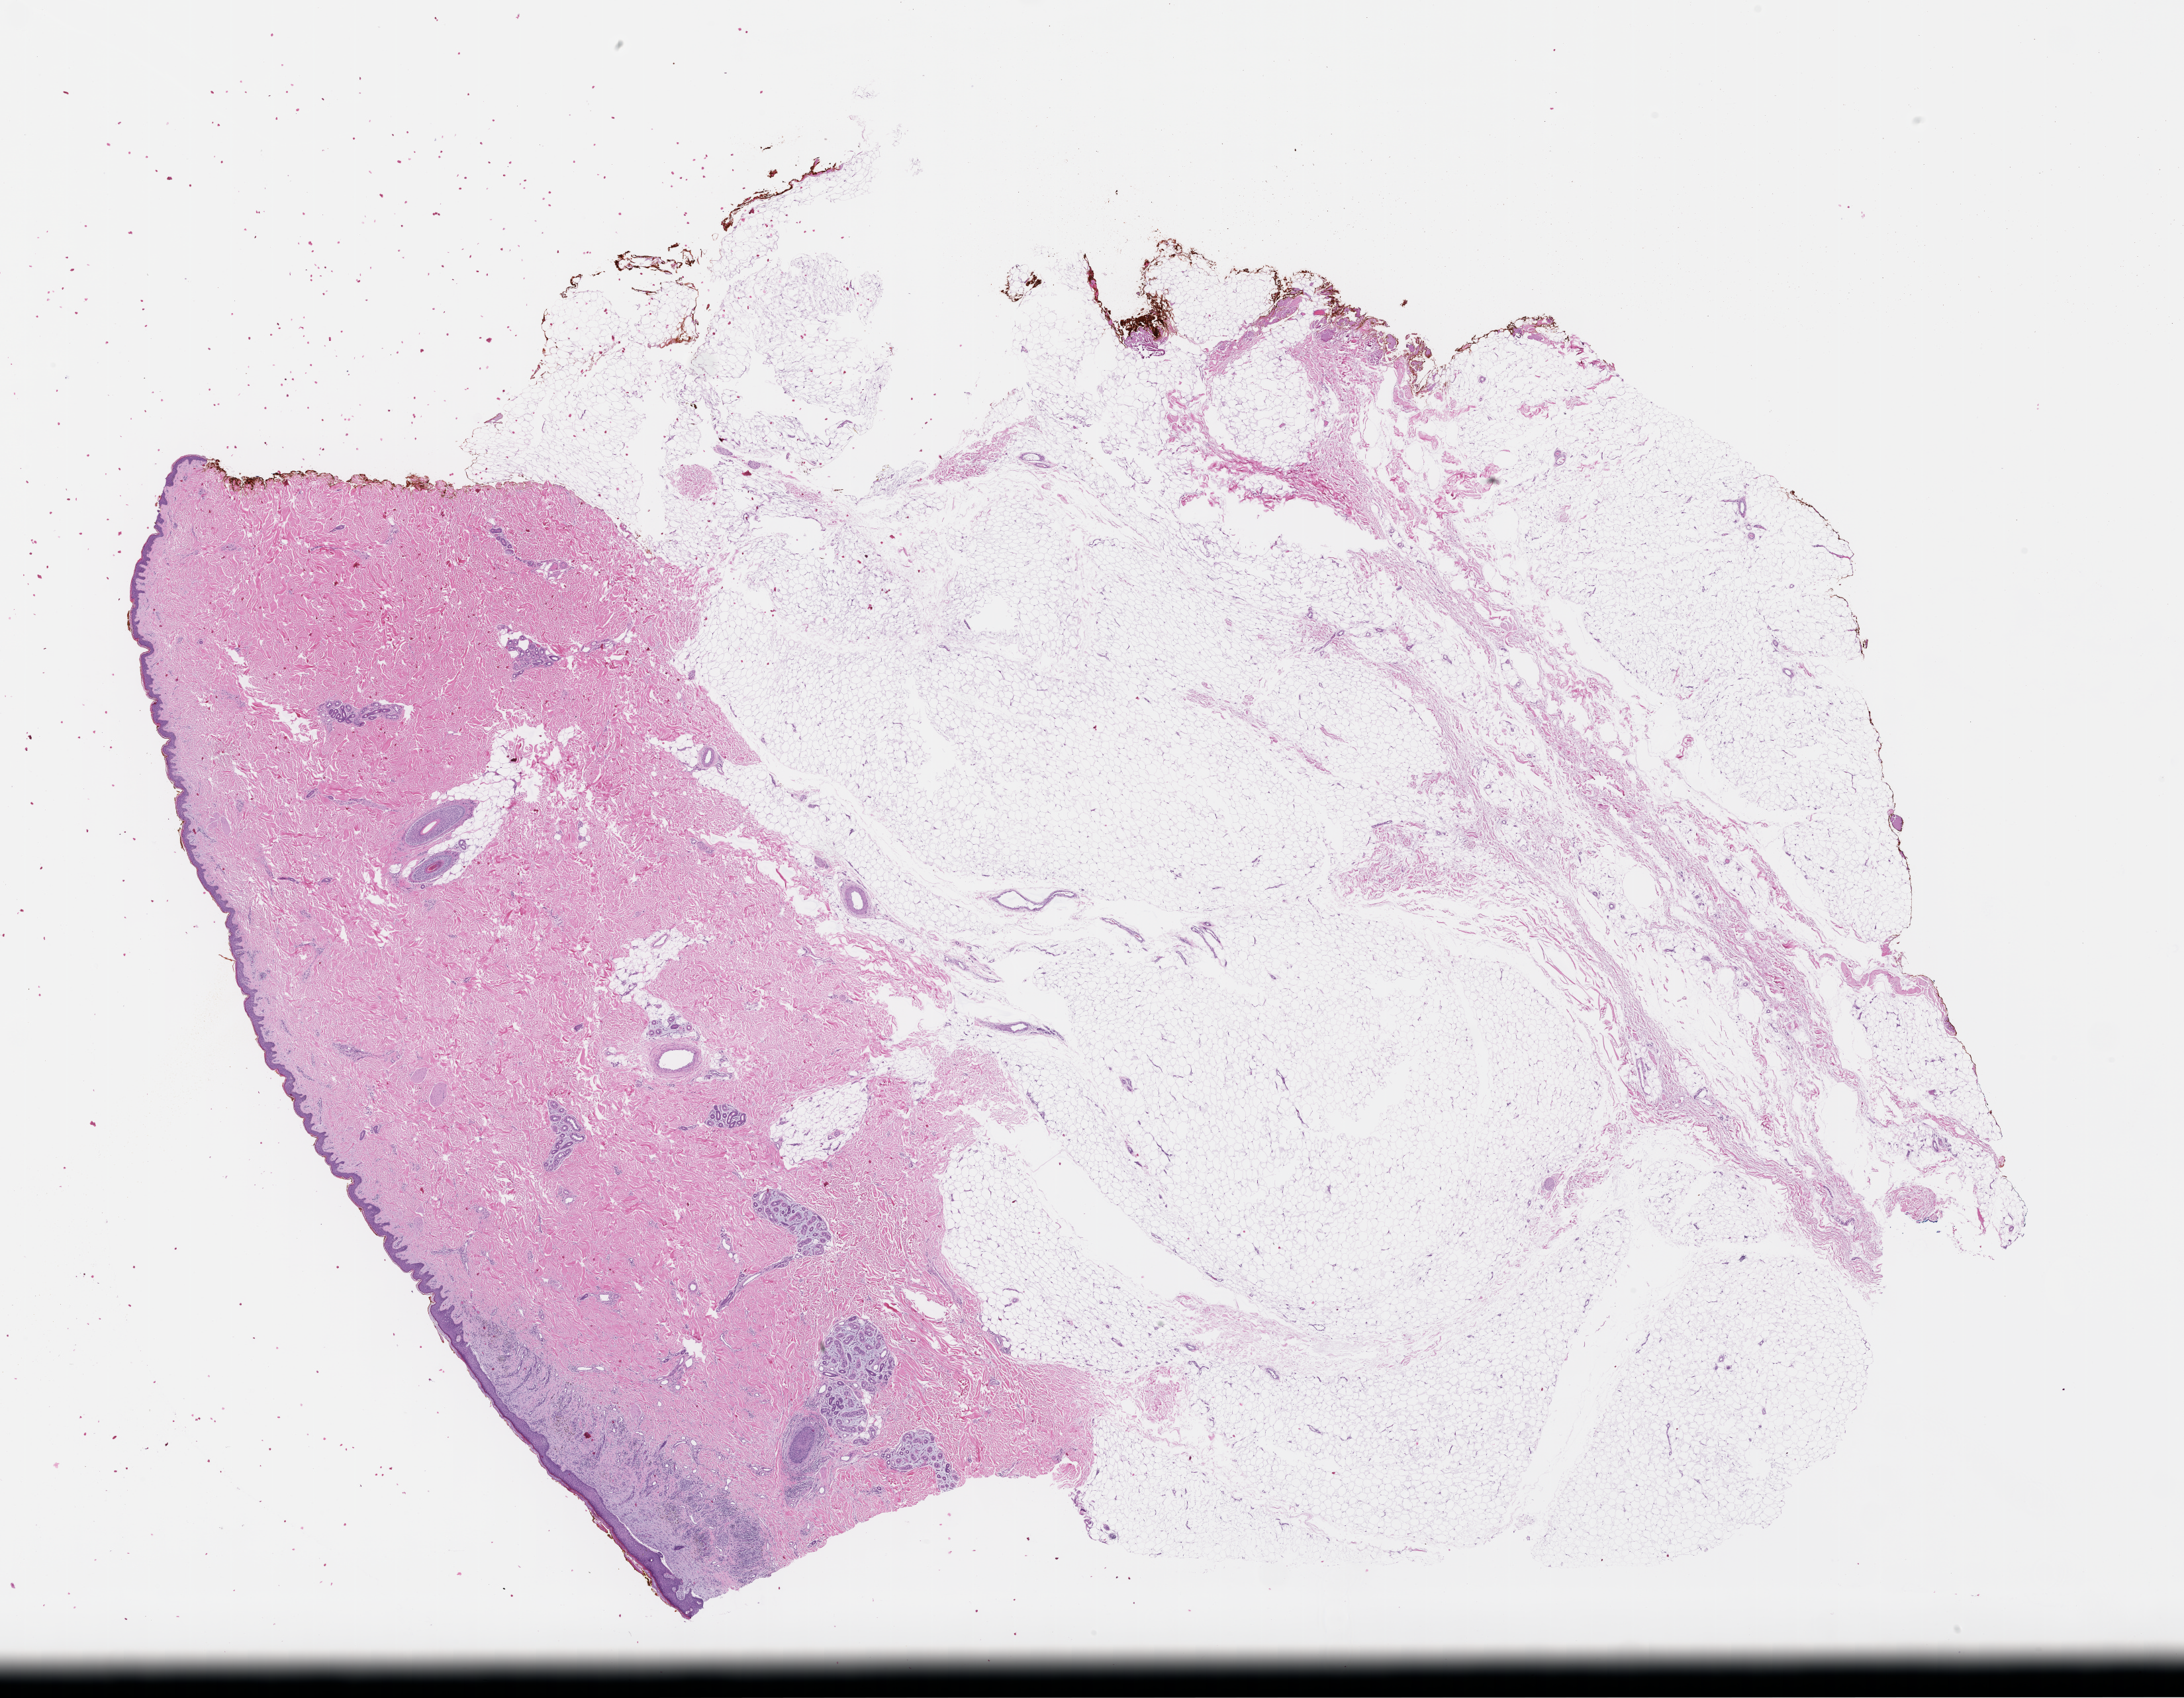
Whole-slide image, H&E stain — a low-resolution overview of the entire scanned area, about 26.6 x 20.7 mm; formalin-fixed paraffin-embedded section; site: skin; collected at baseline (before treatment). Patient: male.
This section: primary tumour tissue. Diagnosis: Melanoma.